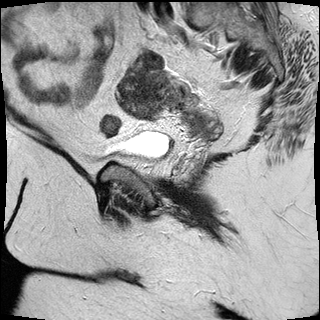
Pelvic MRI for cervical cancer, one sagittal slice. Position 10 of 30 along the scan axis. T2-weighted. 1.5 T. TE 89 ms, TR 2930 ms. 320 × 320 image matrix. Patient: female, 53 years.
Outlined on this slice (expert manual segmentation):
- uterus and cervix: box from (x=115, y=50) to (x=216, y=137) px